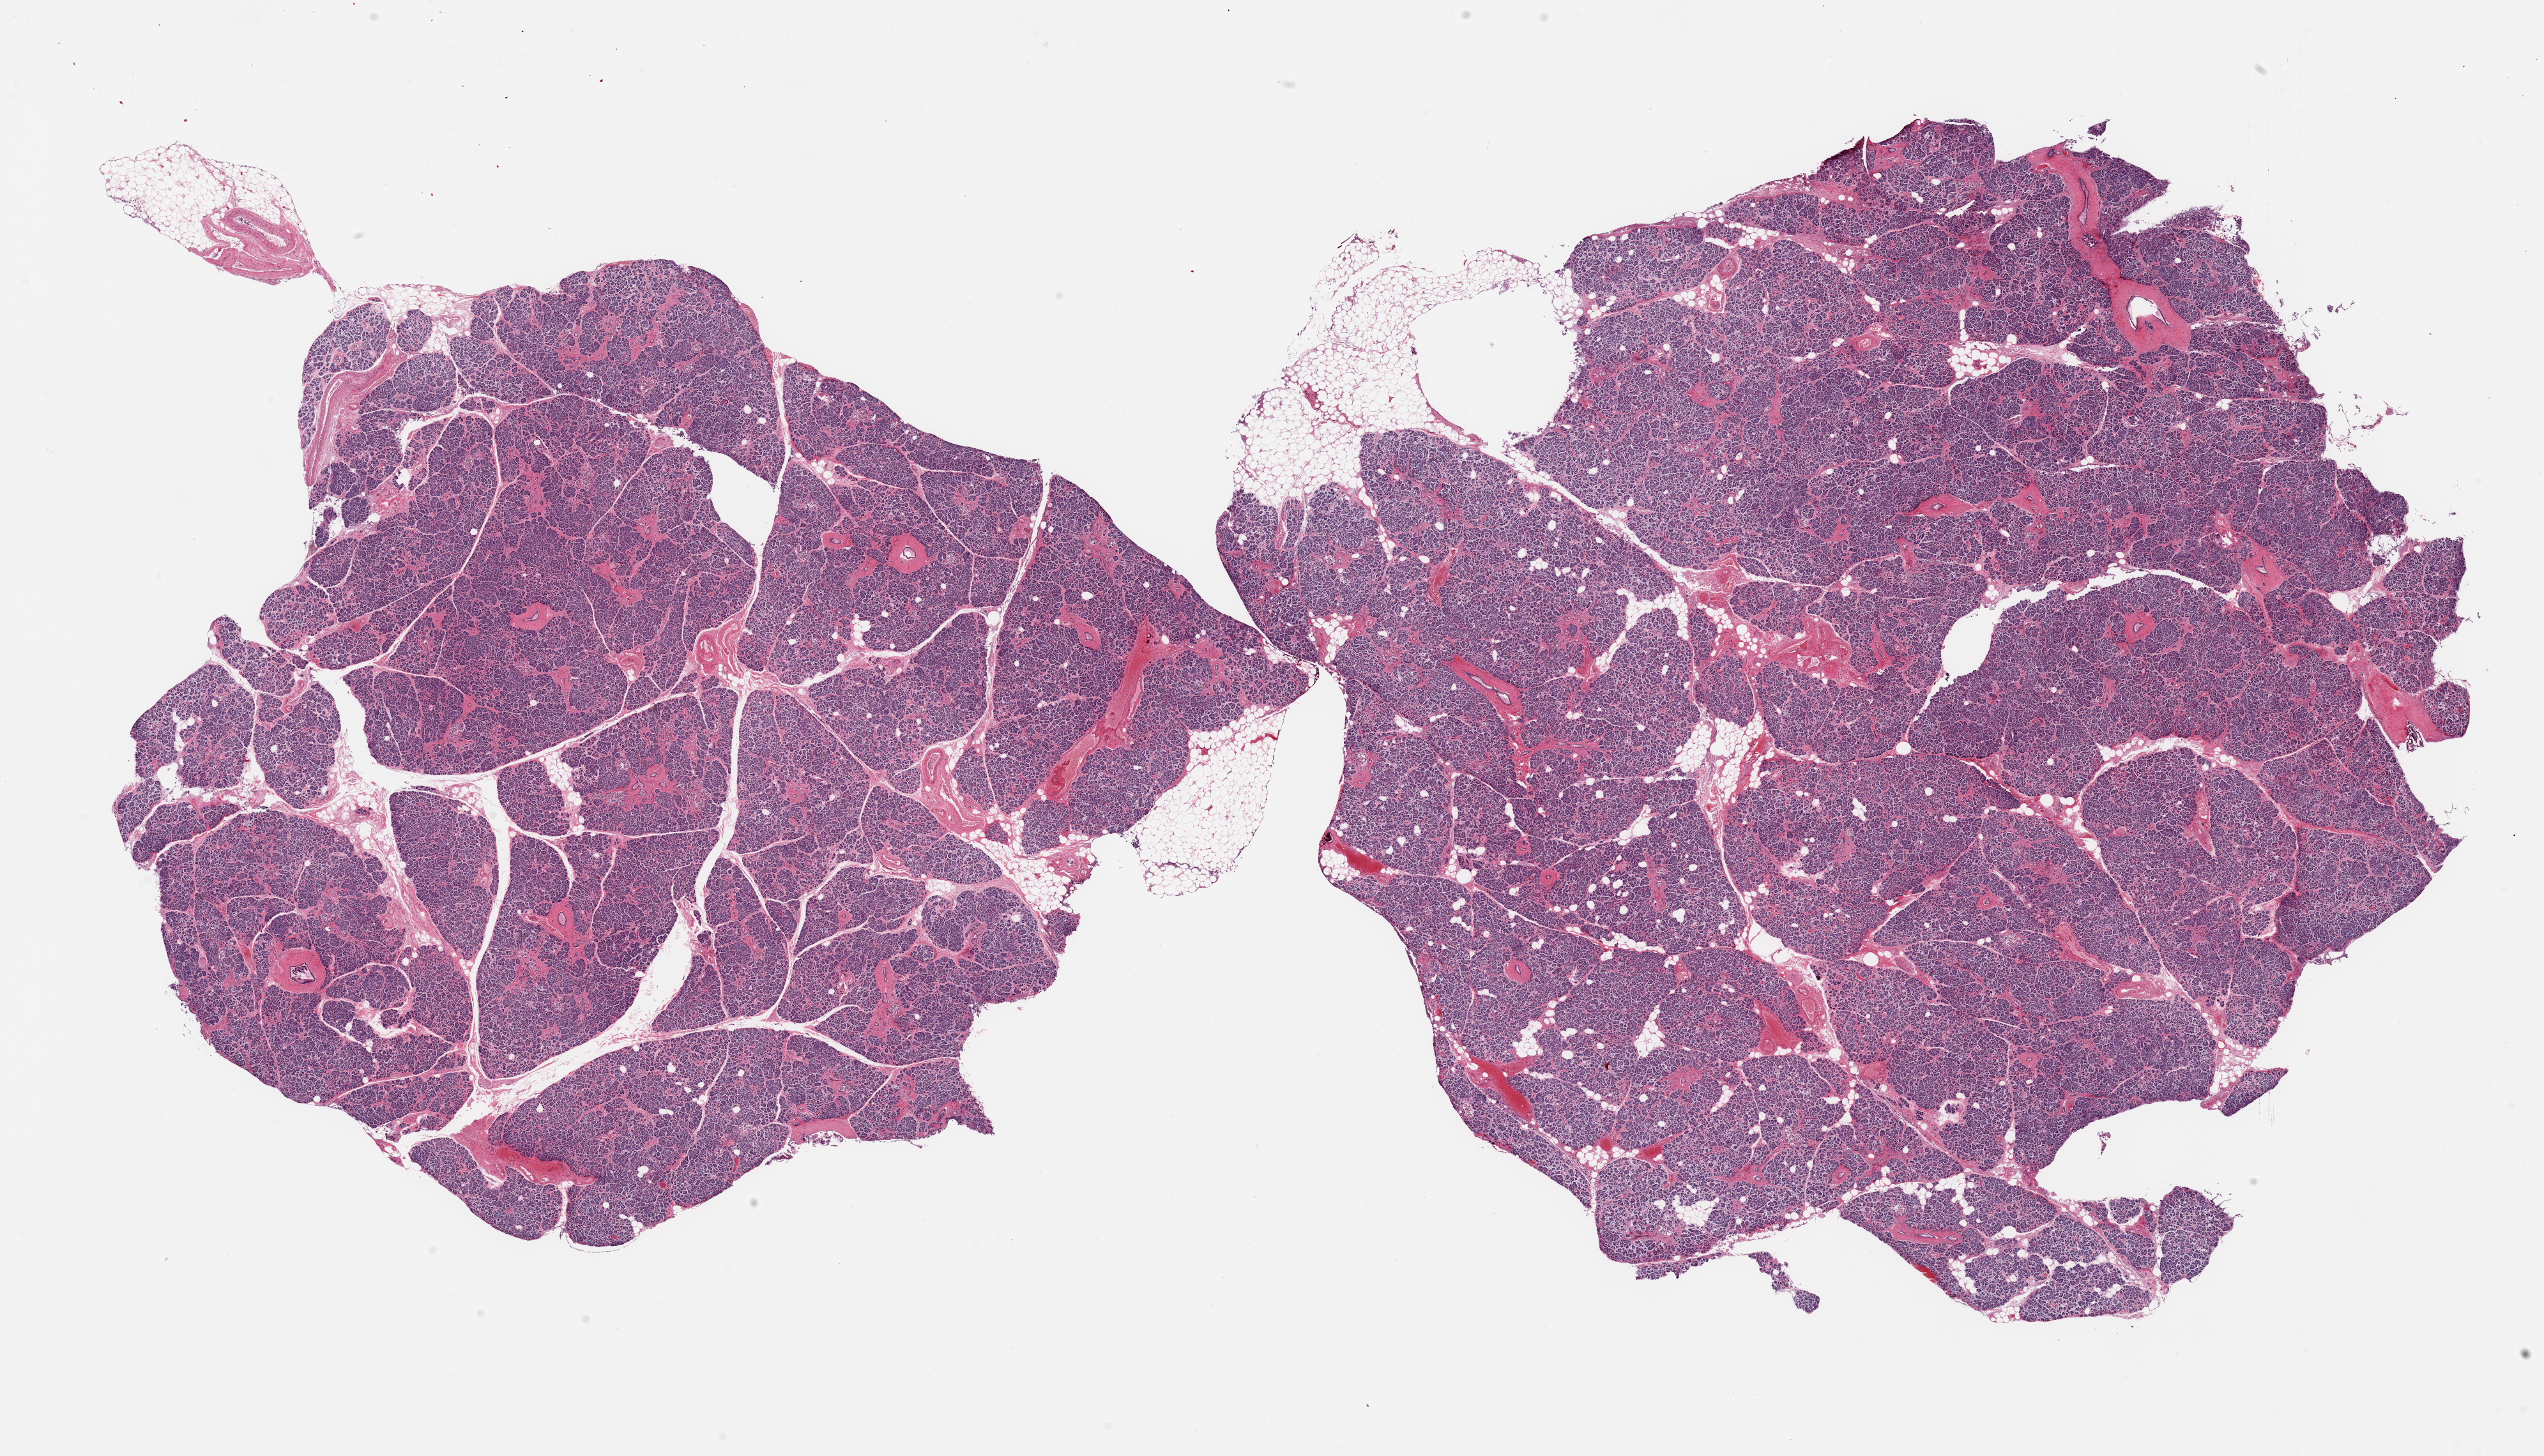
Digitized H&E-stained section, brightfield, a low-resolution overview of the entire scanned area, about 31.5 x 18.0 mm, PAXgene-fixed paraffin-embedded (PFPE) section, target tissue: pancreas, donor tissue sample. Male donor.
Reviewer comment on this tissue sample: 2 pieces; some areas are moderately autolyzed; mild to moderate interstitial and periductal fibrosis.